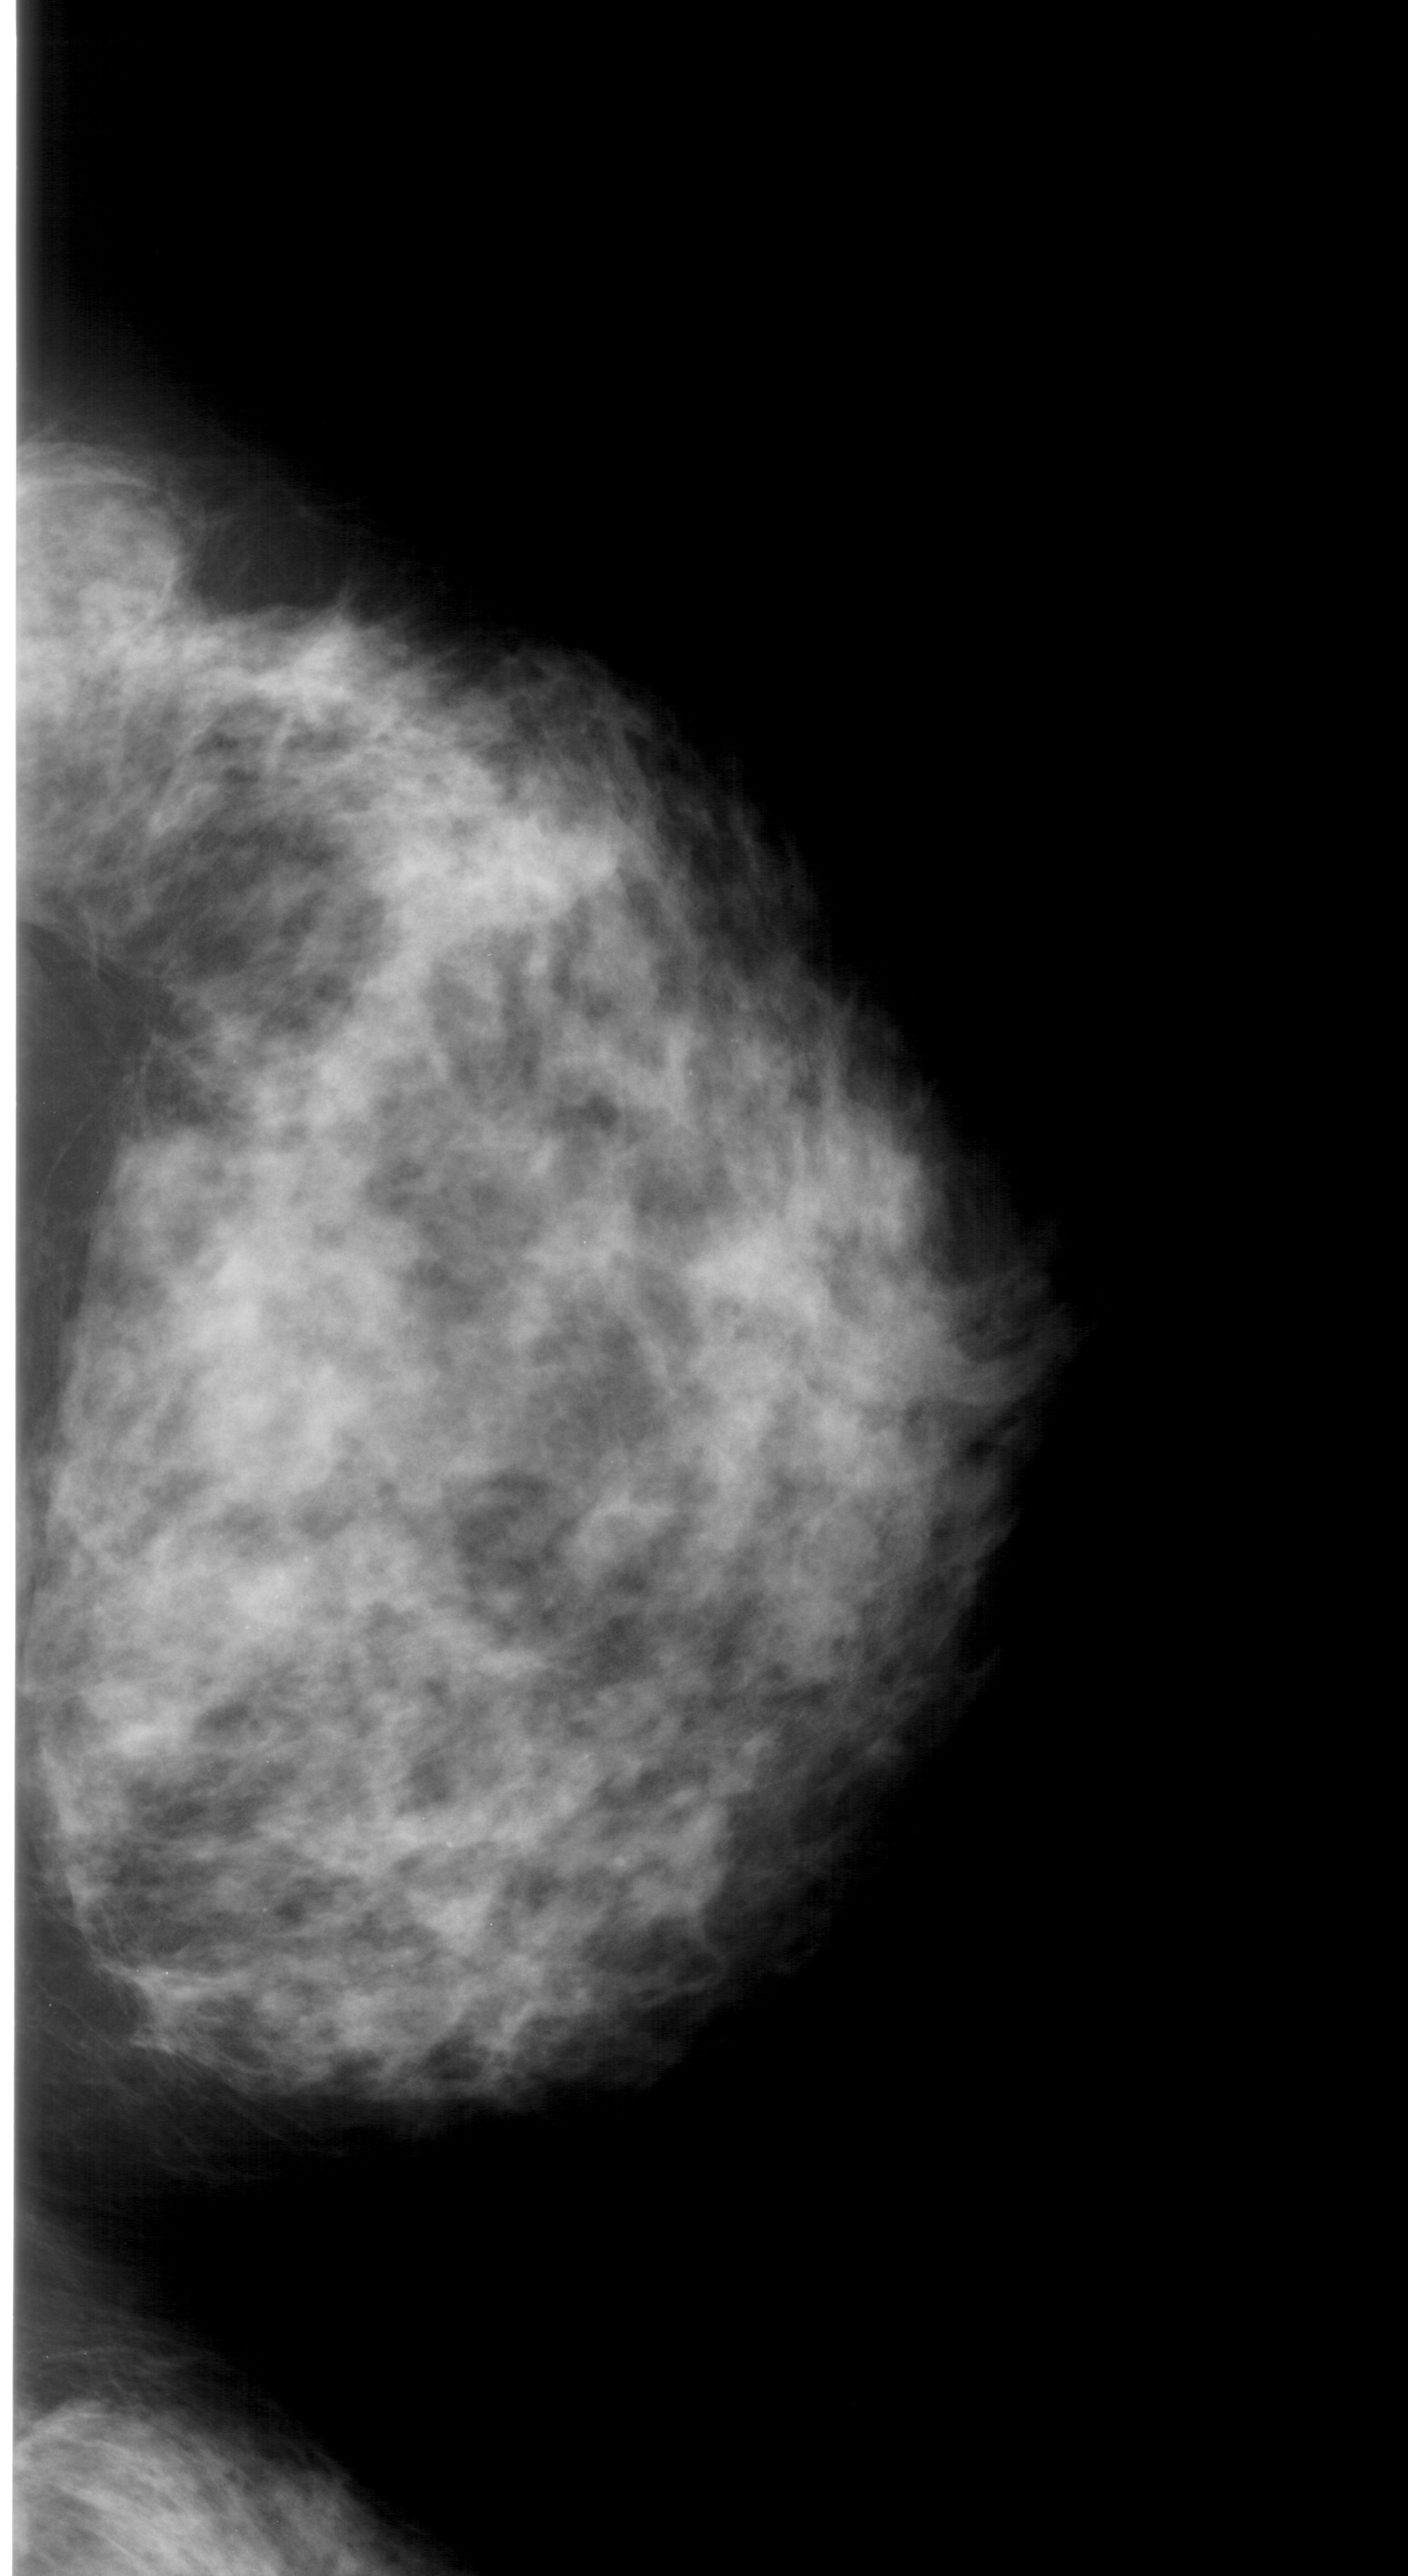
Scanned film-screen mammogram. Right breast. CC view. 1408 × 2576 image matrix.
Marked abnormalities (boxes around the expert regions of interest):
- calcifications, morphology pleomorphic, distribution clustered; BI-RADS assessment category 4; pathology (as recorded): benign: box from (x=173, y=1505) to (x=313, y=1663) px